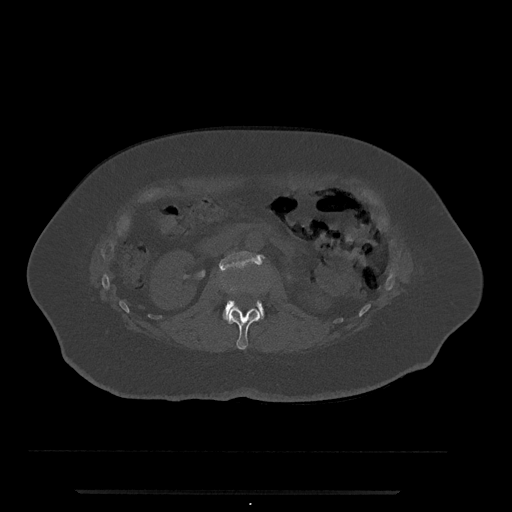
CT including the spine, one axial slice; position 71 of 797 along the scan axis; 120 kVp; bone window (W 1800 / L 400 HU); 512 × 512 image matrix, field of view 440 × 440 mm. Patient: female, 51 years. Case-level facts recorded for this patient, not image findings: primary cancer: neuro; vertebrae with lytic lesions (as recorded): T8.
Annotated regions visible in this slice (semi-automatically segmented with operator editing):
- L1 vertebra: bounding box (x1, y1, x2, y2) in pixels: (223, 308, 261, 350)
- L2 vertebra: (219, 251, 265, 319)